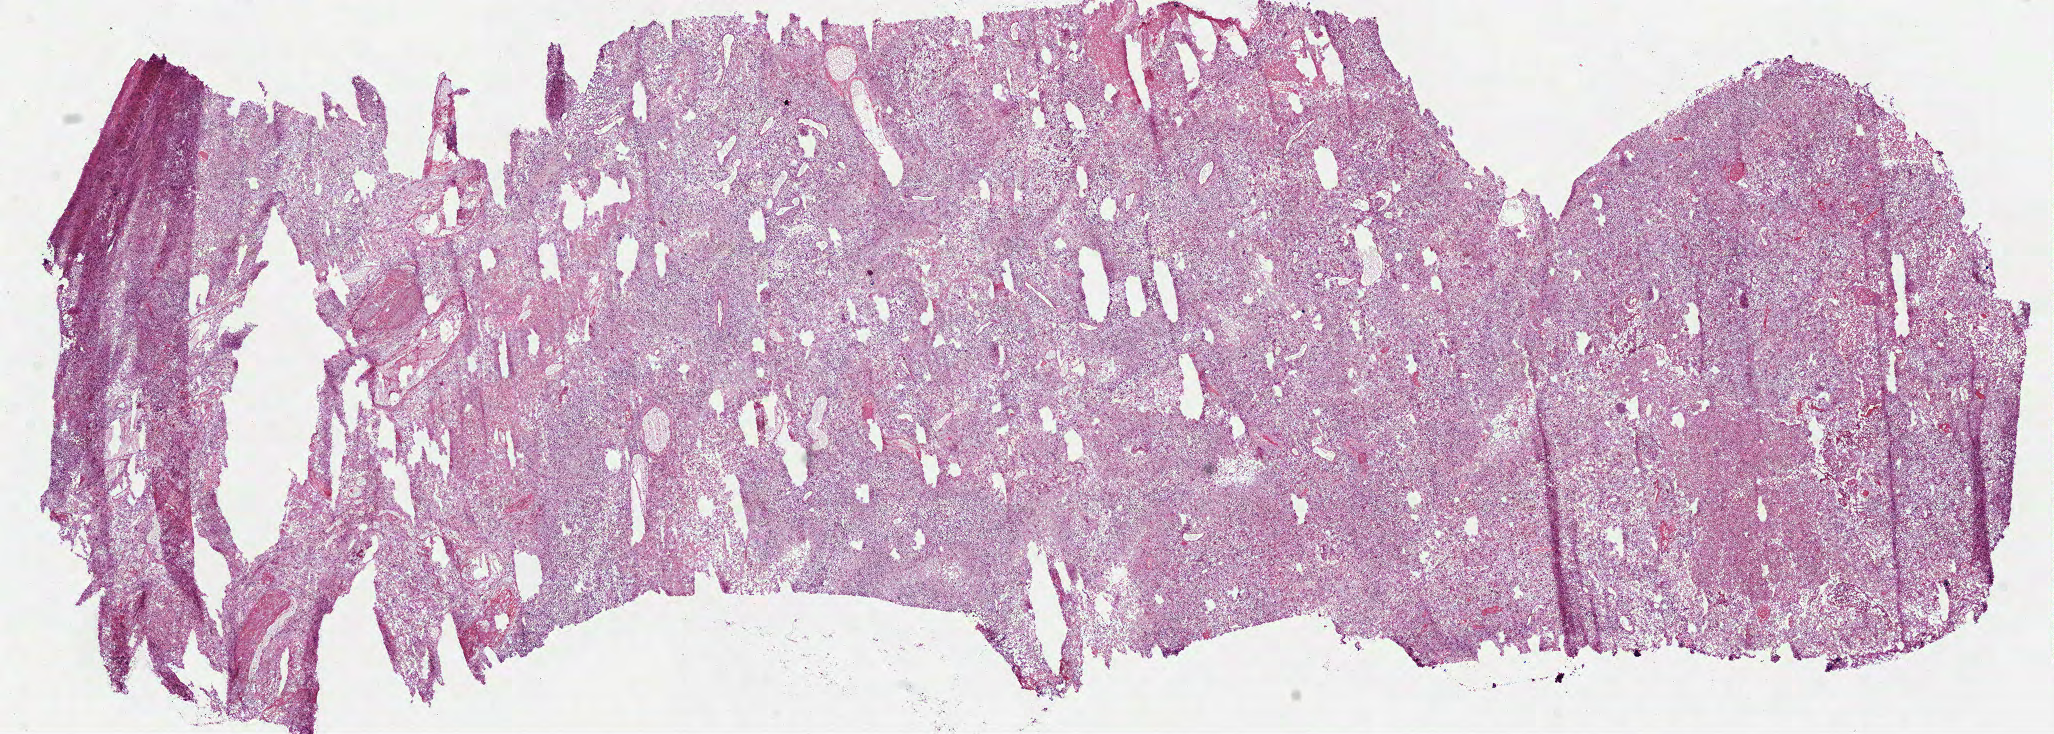
H&E whole-slide image — shown as a low-resolution overview of the whole scanned area (about 16.6 x 5.9 mm). Frozen section. Primary tumour sample from the brain. Female patient; age at initial diagnosis 73 years. Pathologist review of this section (percent, as recorded): tumour cells 90%, tumour nuclei 85%, normal cells 0%, stromal cells 0%, necrosis 10%.
Pathologic diagnosis: Glioblastoma.